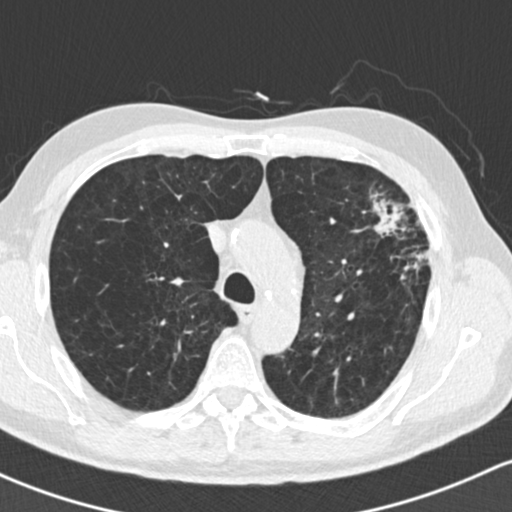
Chest CT (low-dose screening protocol), one axial image. First (baseline) screen. Lung window (W 1500 / L -600 HU). 2 mm slice thickness. Slice 50 of 162 in the series. 512 × 512 image matrix. Male participant, aged 61 years at enrolment. Former smoker at enrolment.
- Expert-annotated lung lesion, bounding box (x1, y1, x2, y2) in pixels: (352, 183, 444, 287).
- Screening reader's record for this exam (one nodule recorded; not confirmed to be the boxed lesion): non-calcified nodule or mass ≥4 mm, left upper lobe, 35 × 35 mm, spiculated (stellate) margins, soft tissue attenuation.
- Official screen result: positive, change unspecified: nodule(s) >= 4 mm or enlarging nodule(s), mass(es), or other non-specific abnormalities suspicious for lung cancer.
- Later outcome: lung cancer diagnosed 19 days after this screen — adenocarcinoma, NOS, left upper lobe, well differentiated (G1), stage IIIA (AJCC 6th edition), 45 mm at pathology.